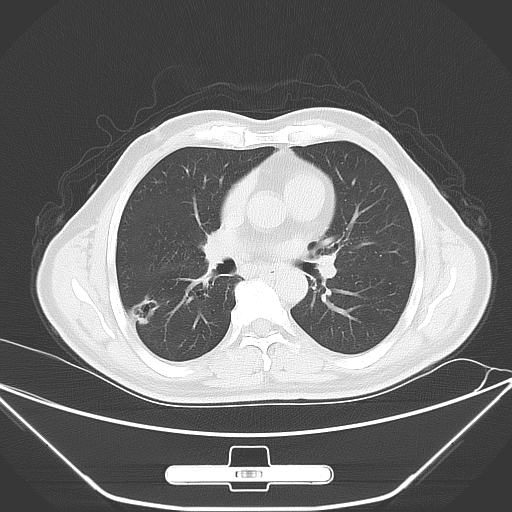
Chest CT, one axial slice; position 31 of 62 along the scan axis; lung window (W 1500 / L -600 HU); 5 mm slice thickness; 512 × 512 image matrix, field of view 398 × 398 mm. Patient: male, 71 years. Case-level facts recorded for this patient, not image findings: clinical TNM (as recorded): T1c N0 M0; histopathological grade: G2.
Structures marked on this image (bounding box drawn by a radiologist):
- lung tumour (recorded histology: adenocarcinoma): bounding box (x1, y1, x2, y2) in pixels: (128, 289, 163, 333)